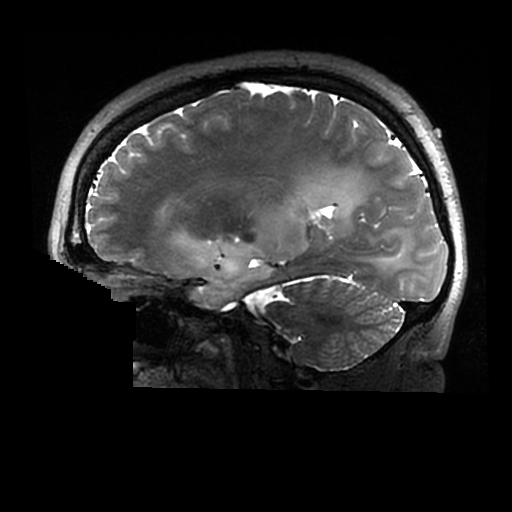
Brain MRI from a brain-tumour surgery series, one sagittal slice. 0.6 mm slice thickness. 512 × 512 image matrix. Case-level facts recorded for this patient, not image findings: histopathology: Astrocytoma; WHO grade: 2; IDH mutation: yes.
Outlined on this slice (expert manual segmentation):
- tumour: bounding box [x1, y1, x2, y2] px = [174, 183, 404, 309]